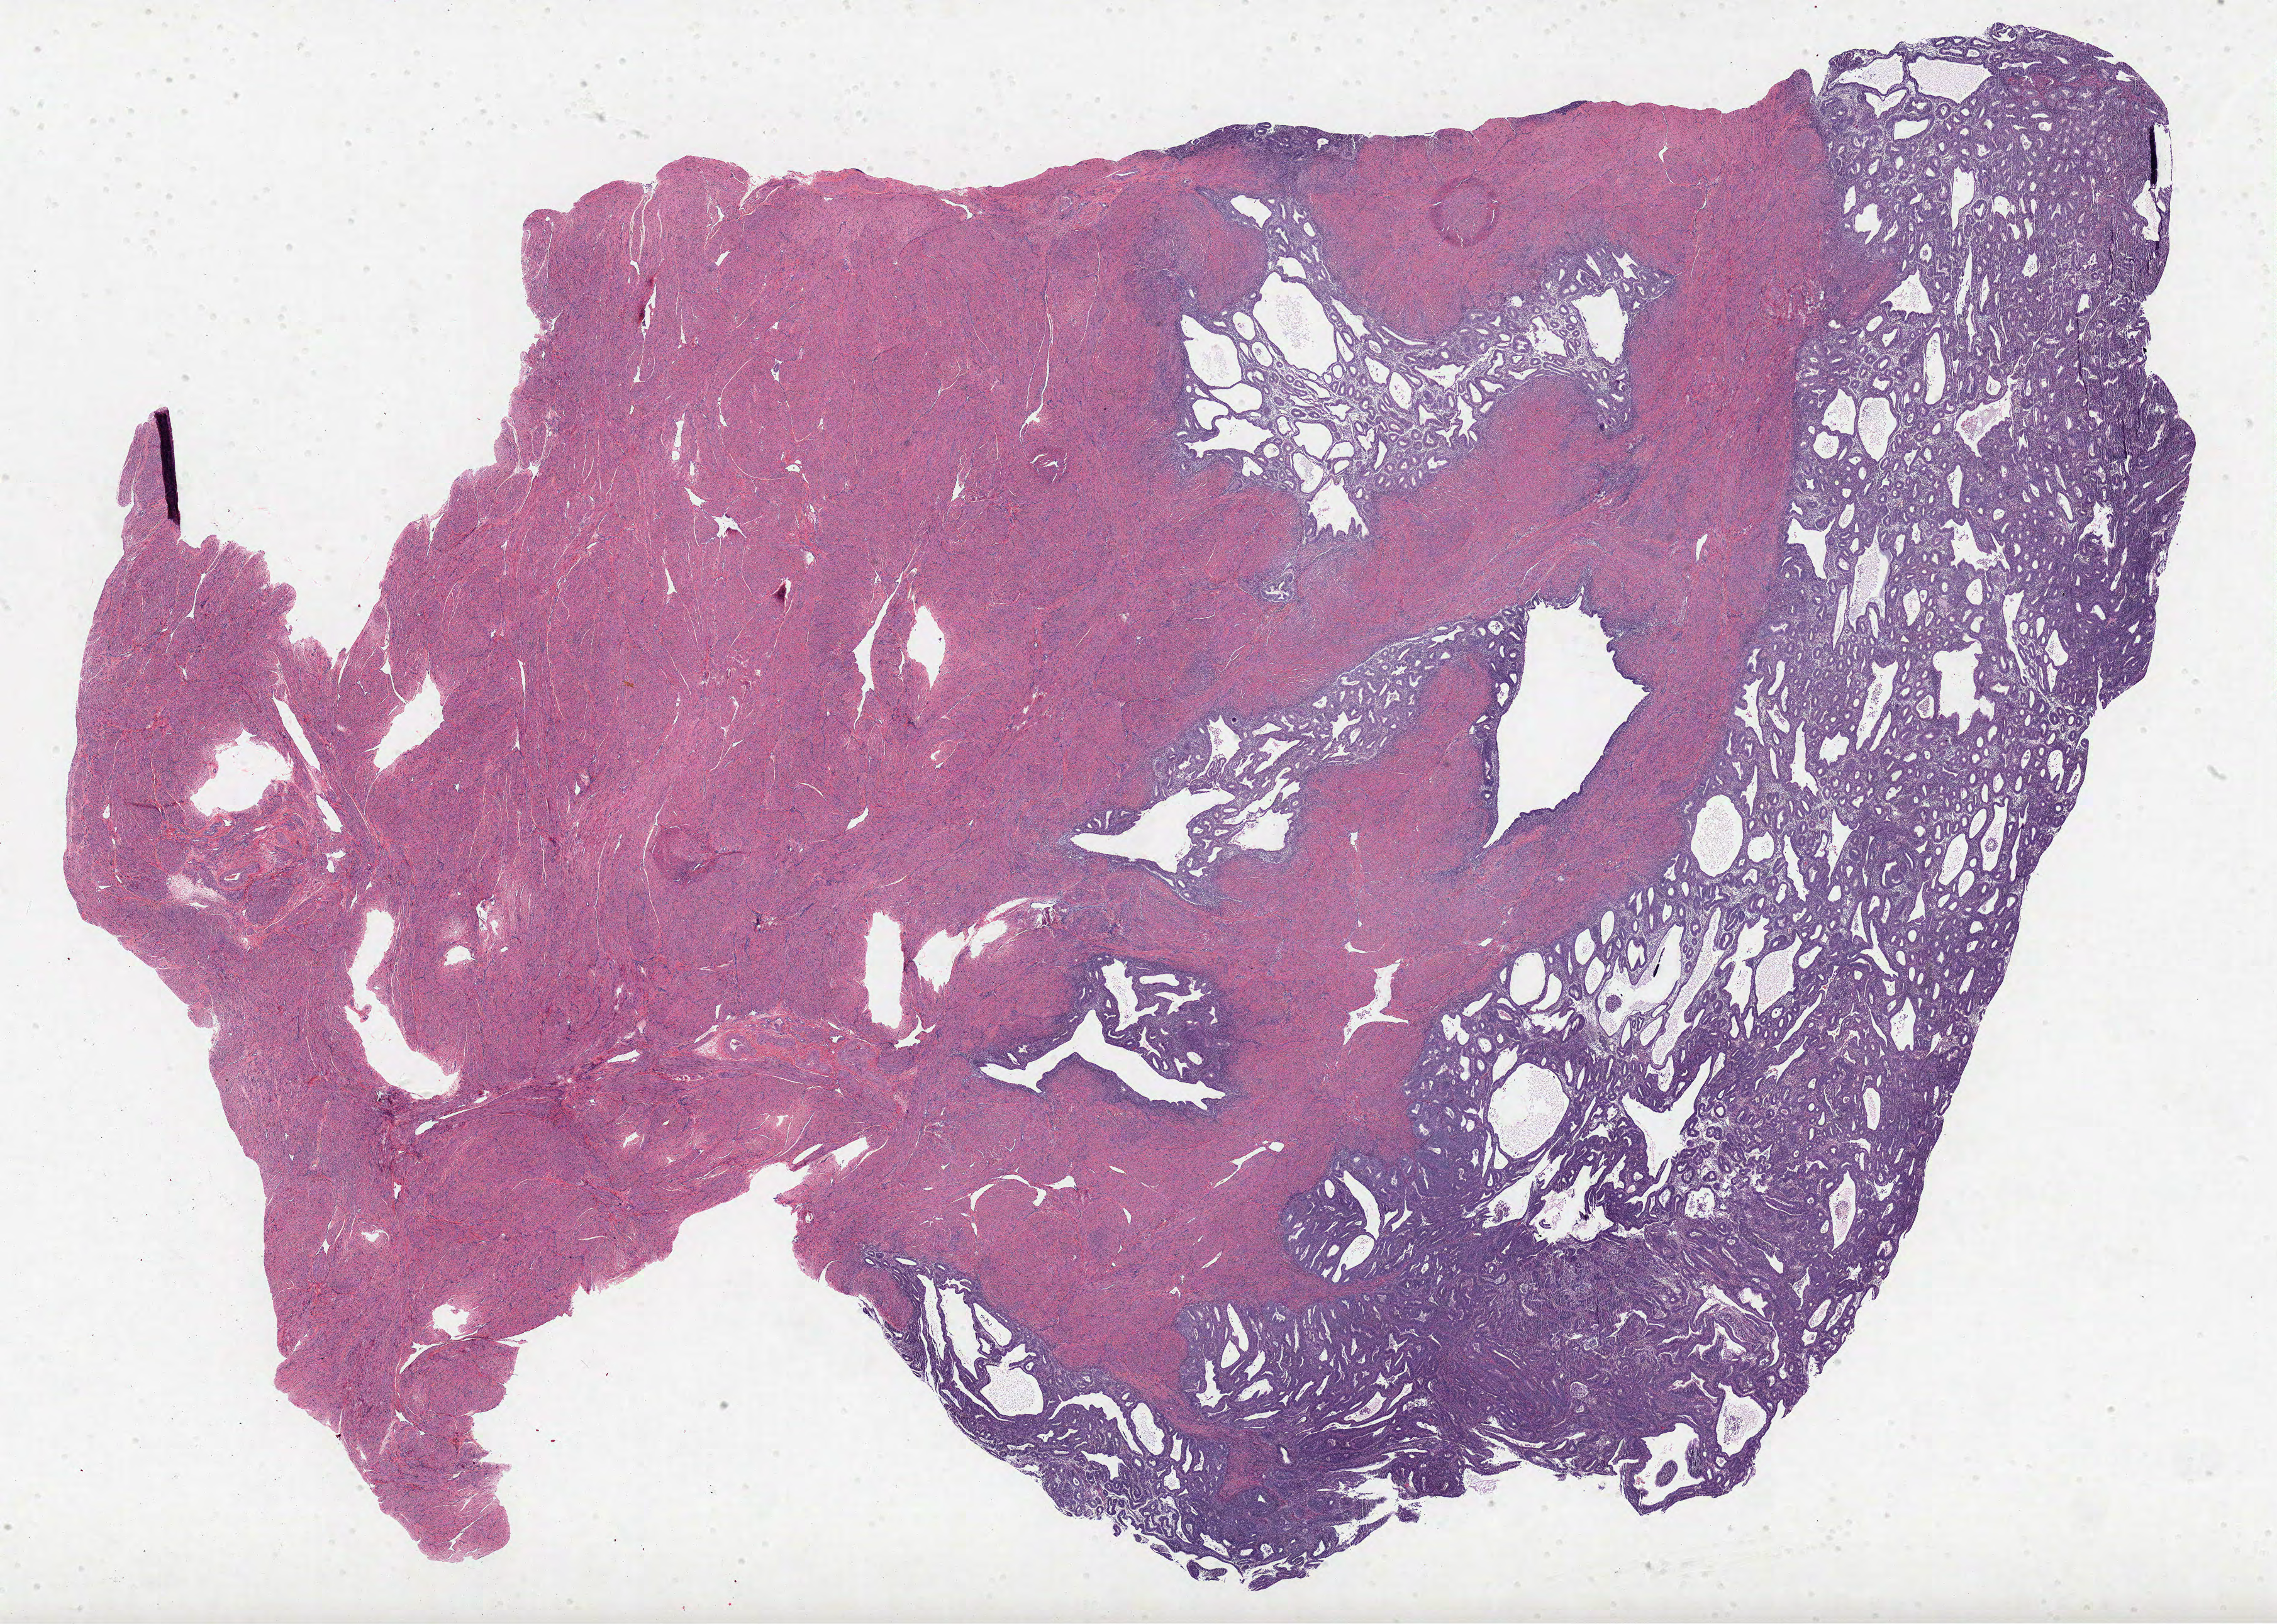
Hematoxylin and eosin (H&E) stained whole-slide image, low-resolution overview of the scanned area, about 28.8 x 20.6 mm, FFPE section, uterus, primary tumour sample. Female patient; age at initial diagnosis 39 years. Histologic grade: G1 (well differentiated).
Diagnosis: Endometrioid adenocarcinoma, NOS (endometrium). Lymph nodes positive (case pathology): 0 of 16 examined. FIGO stage: IA.